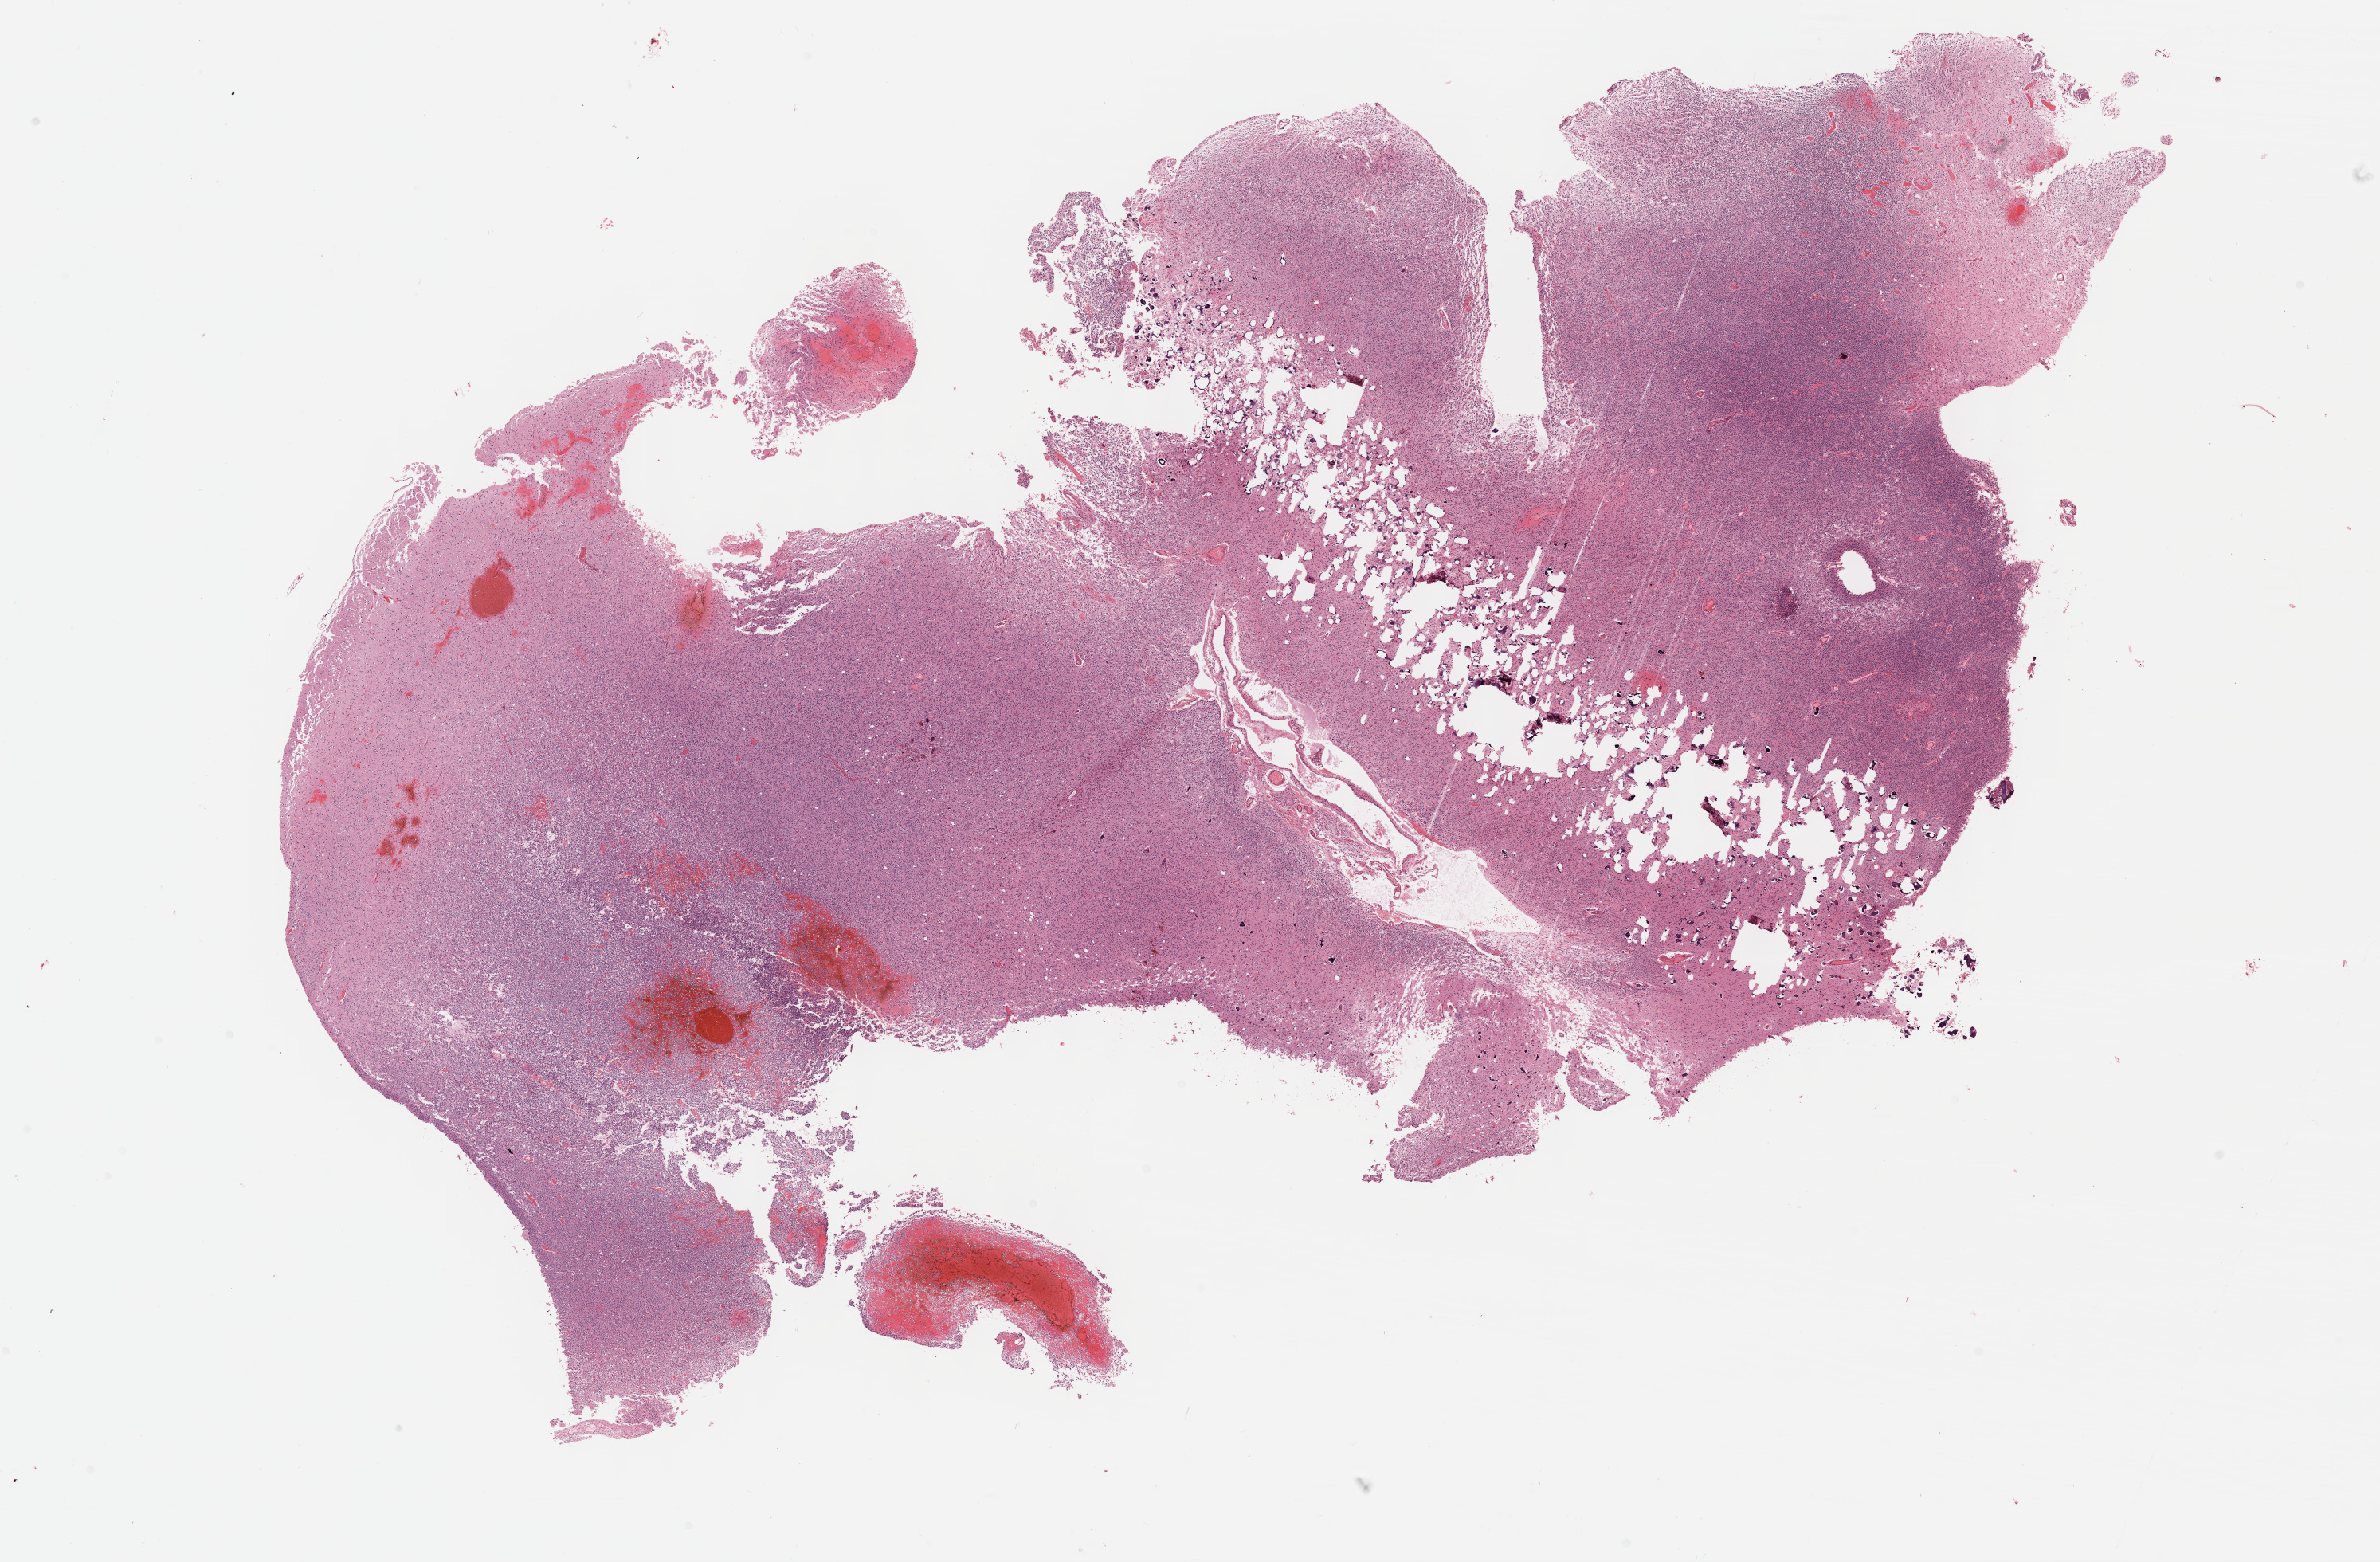
Digitized H&E-stained tissue section (whole slide), shown as a low-resolution overview of the whole scanned area (about 24.2 x 15.9 mm, from a 40x scan), formalin-fixed paraffin-embedded (FFPE) diagnostic section, primary tumour sample from the brain. Patient: male, age at initial diagnosis 40 years. Histologic grade: G3 (poorly differentiated).
* diagnosis: Oligodendroglioma, anaplastic (cerebrum)